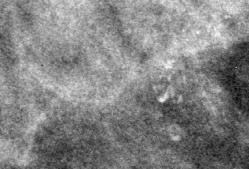
Region of interest cut from a scanned film mammogram (one marked finding), left breast, MLO view.
Marked abnormality: calcifications, morphology pleomorphic, distribution clustered; BI-RADS assessment category 4; subtlety rating 2 on a 1 (subtle) to 5 (obvious) scale; pathology result (as recorded, not read from the image): benign.